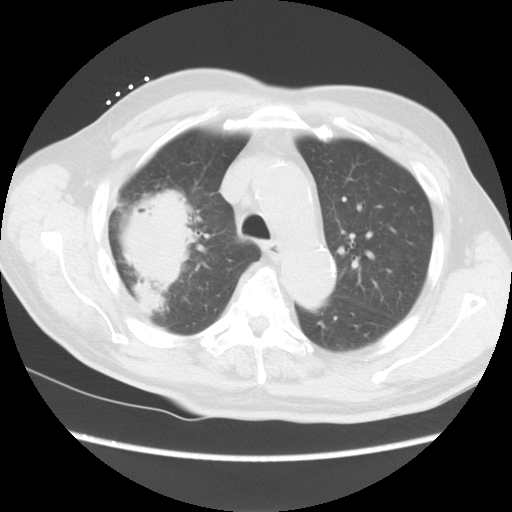
Chest CT, one axial slice. Position 13 of 15 along the scan axis. Reconstruction kernel STANDARD. 120 kVp. Lung window (W 1500 / L -600 HU). 5 mm slice thickness. 512 × 512 image matrix, field of view 350 × 350 mm. Male patient, age 68 years. Case-level facts recorded for this patient, not image findings: clinical TNM (as recorded): T4 N3 M0.
Outlined on this slice (rectangle marked by the reading radiologist):
- lung tumour (recorded histology: squamous cell carcinoma): bounding box [x1, y1, x2, y2] px = [125, 193, 189, 318]